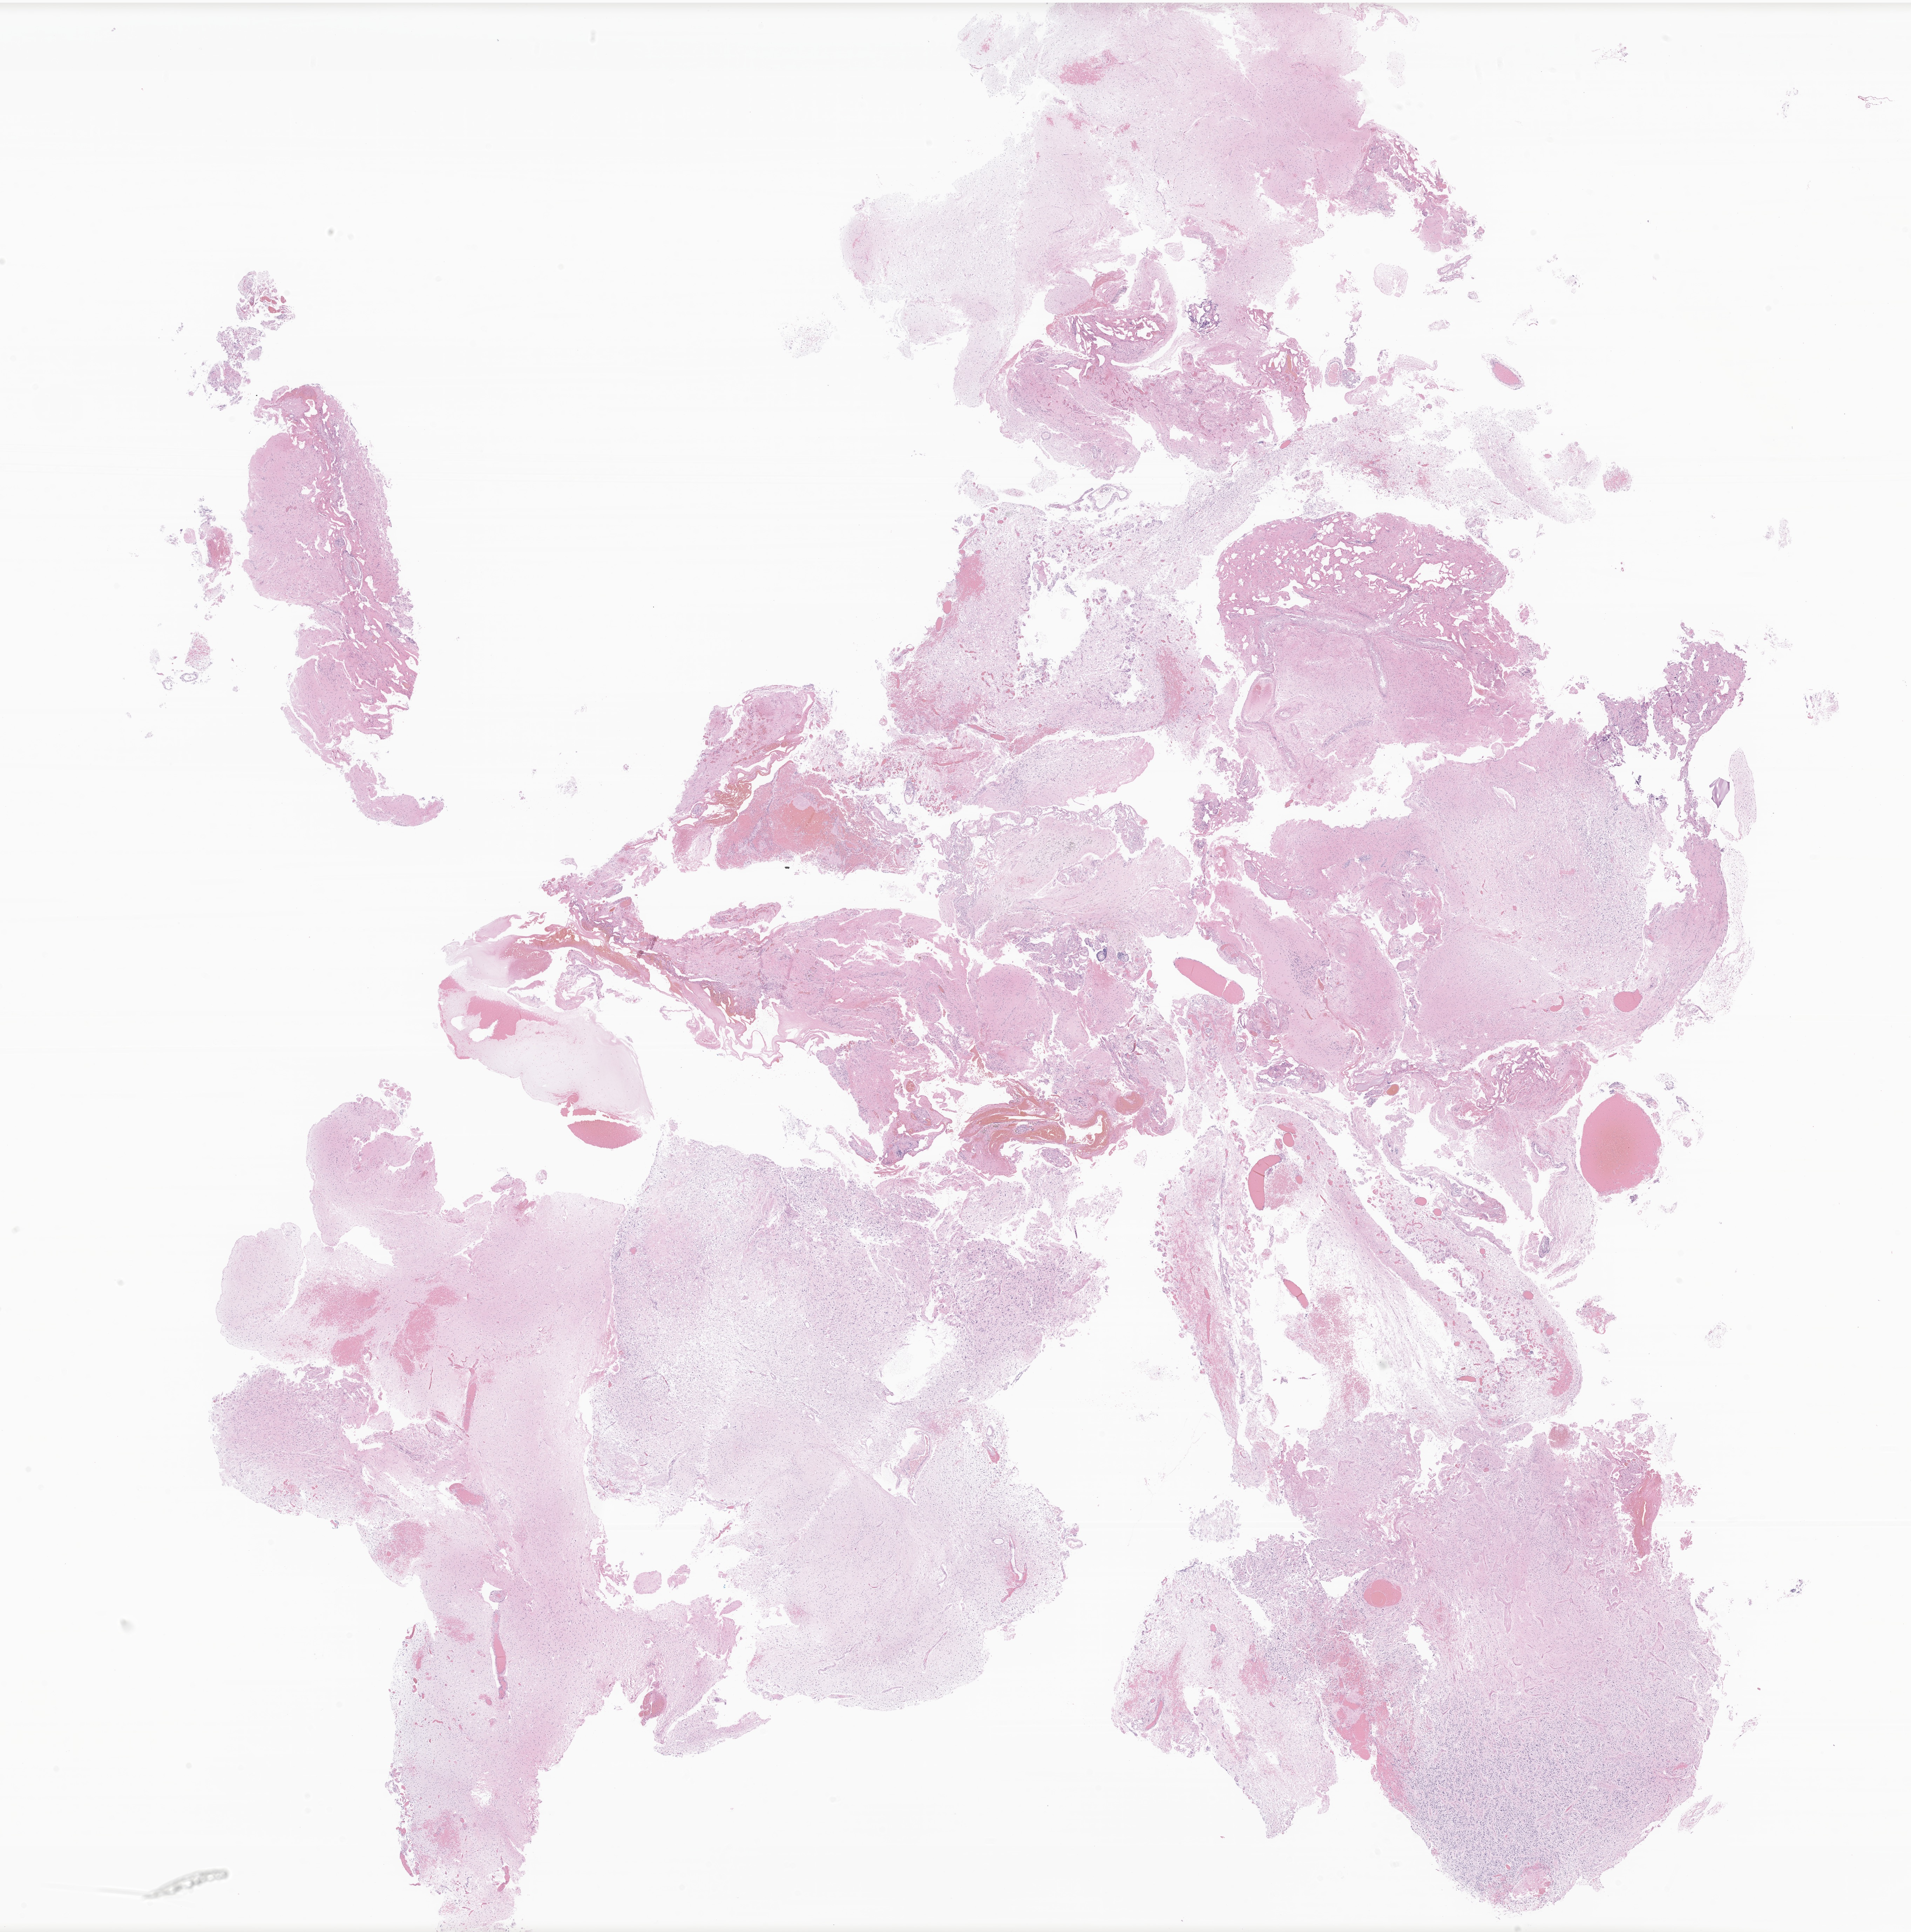
Digitized hematoxylin and eosin (H&E)-stained section of tumor tissue from the brain, whole scanned area (about 23.0 x 23.2 mm) shown as a low-resolution overview; formalin-fixed paraffin-embedded section. Patient male; age 194 months.
• diagnosis (ICD-O-3 morphology term): Pilocytic astrocytoma